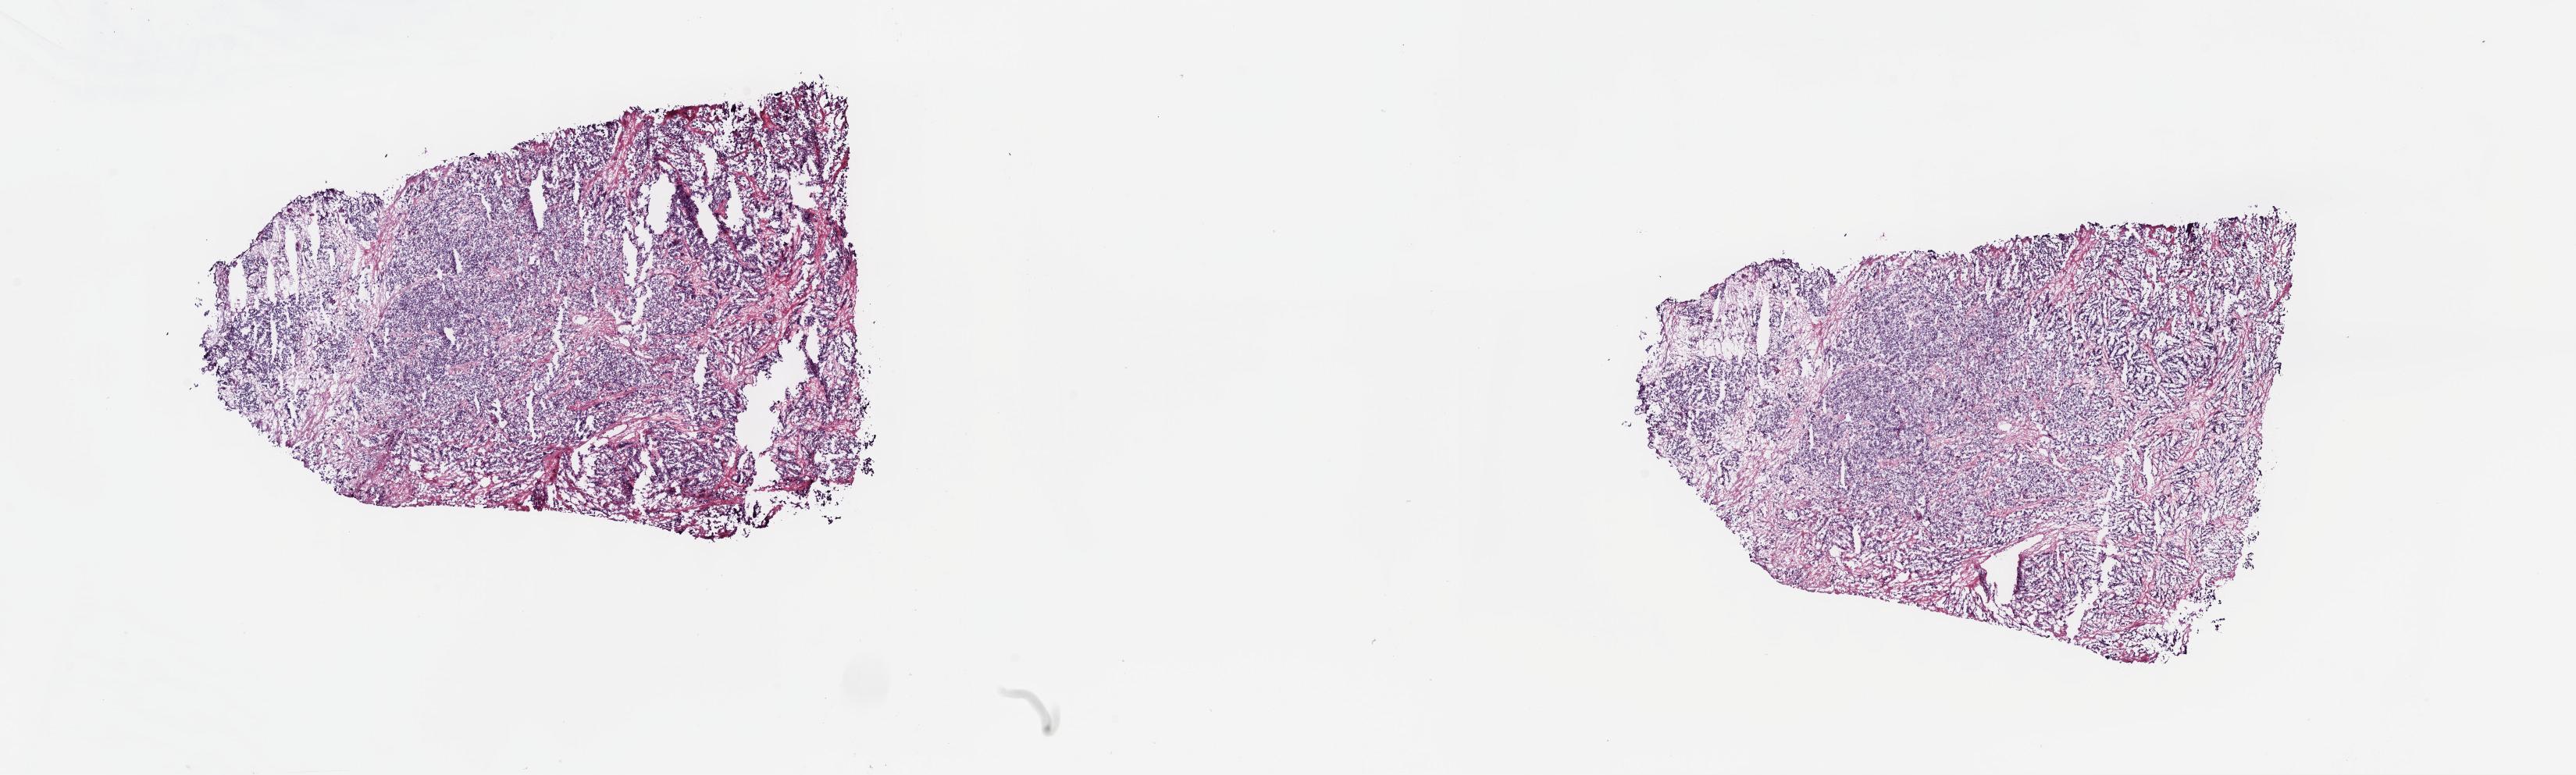
Whole-slide histology image, Hematoxylin and eosin (H&E) stained — low-resolution overview of the scanned area, about 26.7 x 8.0 mm (slide scanned at 40x); frozen section from the top of the tissue portion; primary tumour sample from the testis. Male, age 29 years at initial diagnosis. Composition of this section per pathologist review: tumour cells 70%, tumour nuclei 70%, normal cells 0%, stromal cells 30%, necrosis 0%. Inflammatory infiltration, as recorded: lymphocyte infiltration 0%, monocyte infiltration 0%, neutrophil infiltration 0%.
Laterality: left. Histologic diagnosis: Seminoma, NOS. AJCC pathologic stage: I (7th edition).